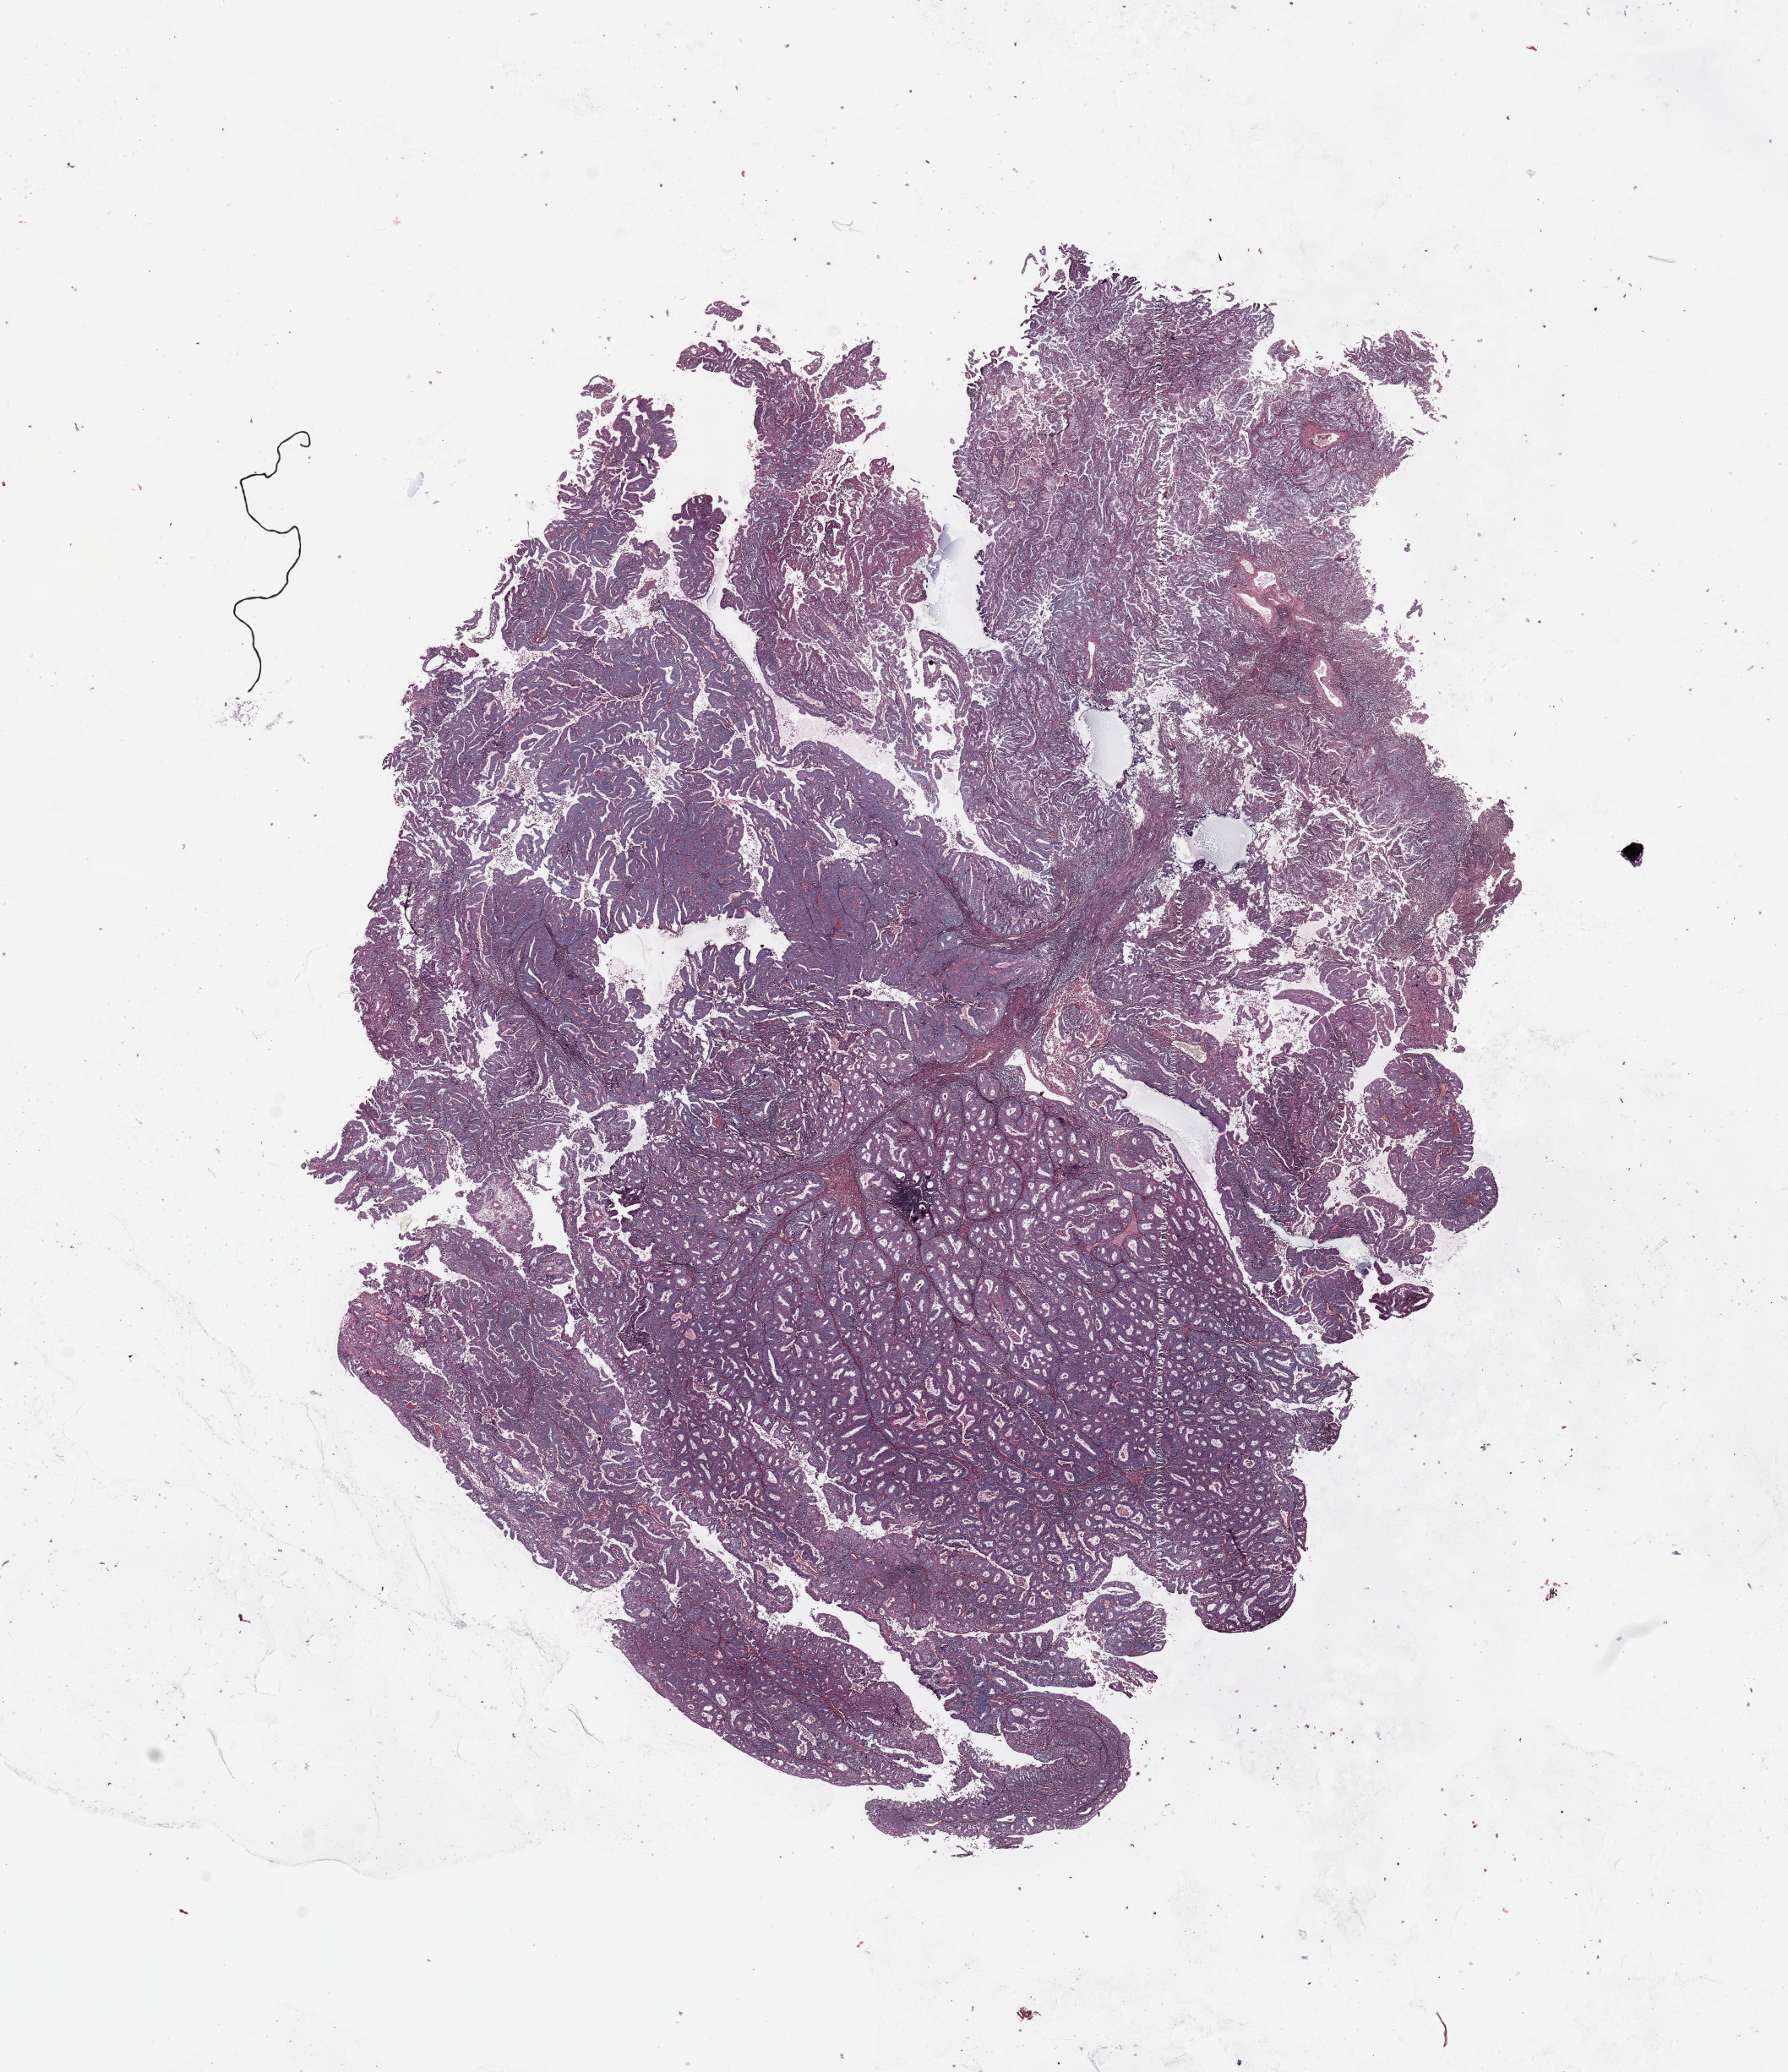
Digitized Hematoxylin and eosin (H&E) stained tissue section (whole slide) — shown as a low-resolution overview of the whole scanned area (about 16.7 x 19.4 mm, from a 20x scan), tumour tissue sample, sampled site: uterus. Patient: female, age 63 years. Histologic grade: G2 (moderately differentiated). Slide review estimates, as recorded: tumour nuclei 90%, necrosis 2%.
AJCC pathologic stage: III. Diagnosis: Endometrioid adenocarcinoma, NOS.